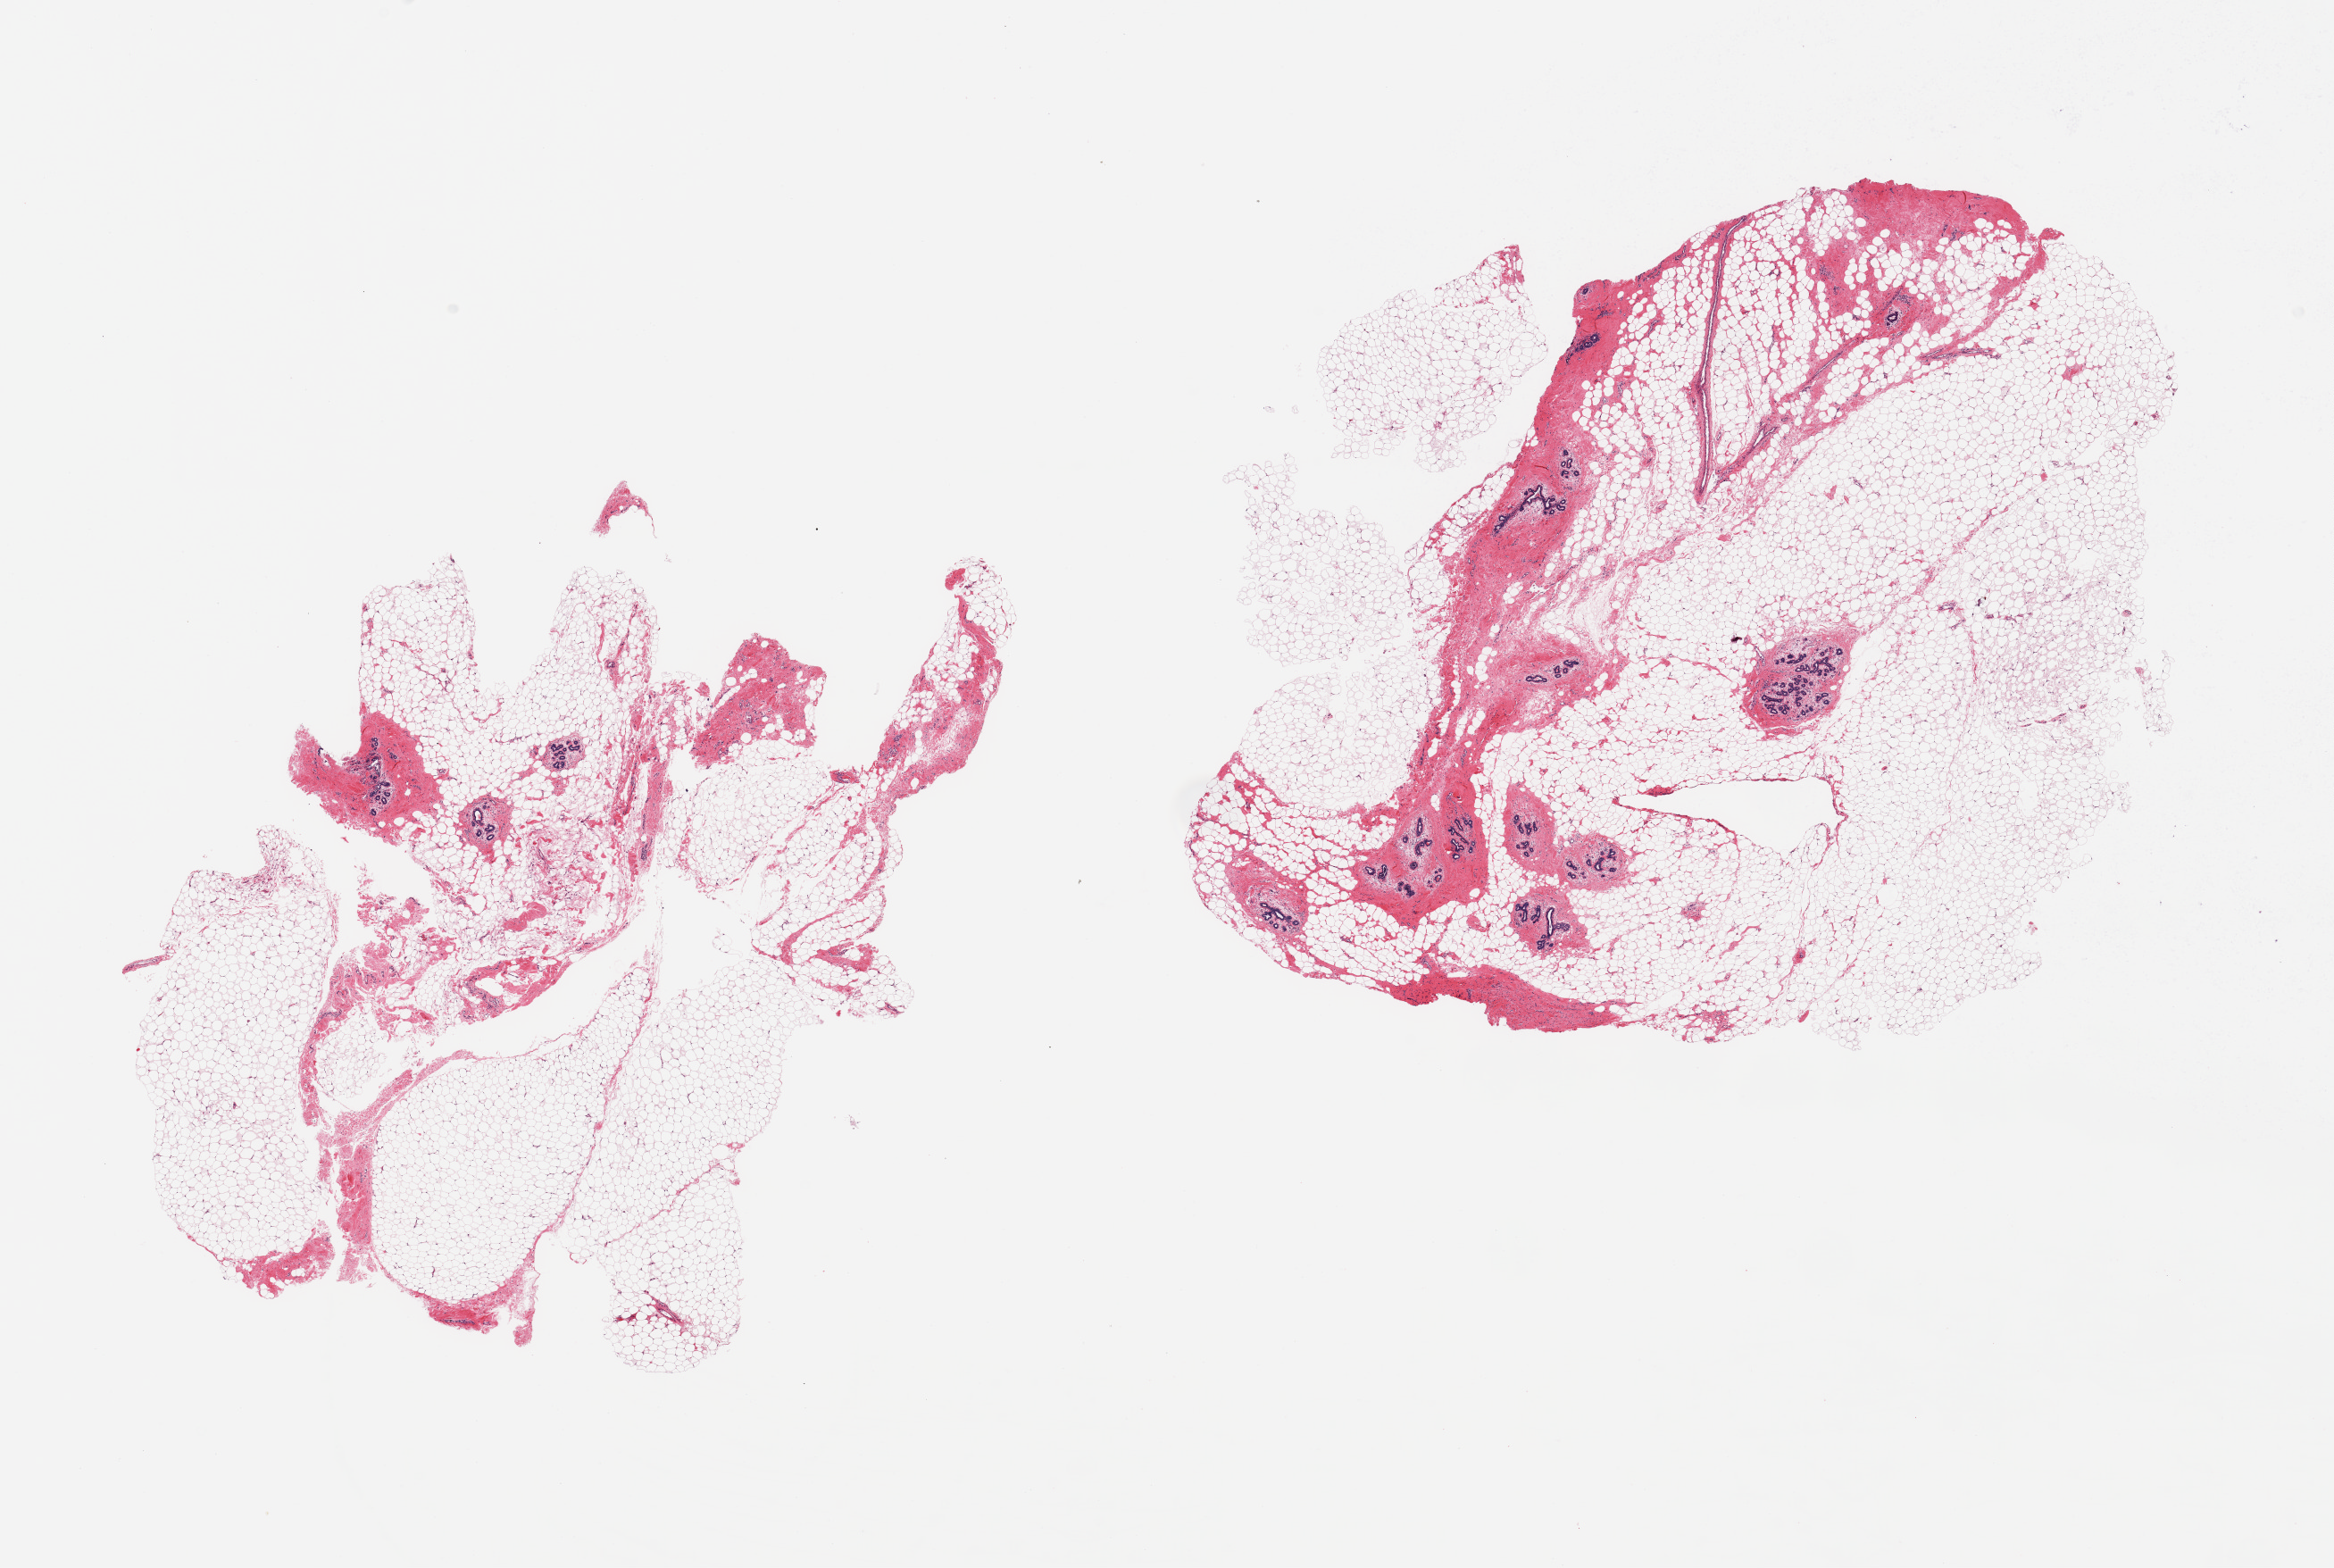
Digitized hematoxylin and eosin (H&E)-stained section — whole scanned area (about 20.7 x 13.9 mm) shown as a low-resolution overview; PAXgene-fixed, paraffin-embedded tissue; sampled site (target tissue): breast; donor tissue sample. Donor sex: female.
* reviewer comment on this tissue sample: 2 pieces; ductal and lobular units present; fat occupies 80%